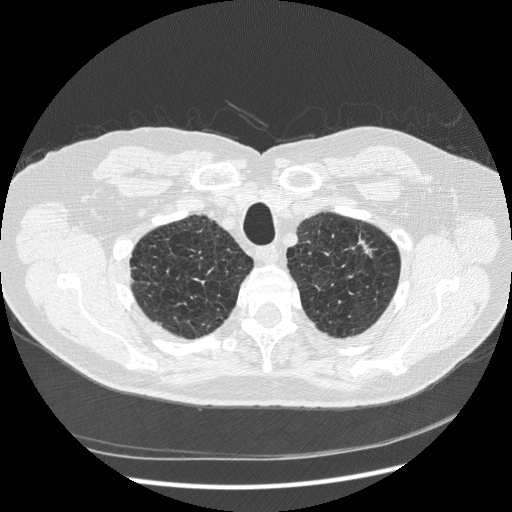
Chest CT (low-dose screening protocol), one axial image, first (baseline) screen, lung window (W 1500 / L -600 HU), 1.25 mm slice thickness, standard (soft-tissue) reconstruction kernel (STANDARD). Male, age 70 years at enrolment.
Lesion marked by an expert reader, bounding box (x1, y1, x2, y2) in pixels: (332, 219, 387, 274). The screening reader recorded 2 non-calcified nodules or masses ≥4 mm on this exam (right lower lobe, right lower lobe); which of them this box marks is not recorded. Later outcome: lung cancer diagnosed 816 days after this screen (after the third annual screen) — squamous cell carcinoma, NOS, left upper lobe, moderately differentiated (G2), stage IA (AJCC 6th edition), 18 mm at pathology.